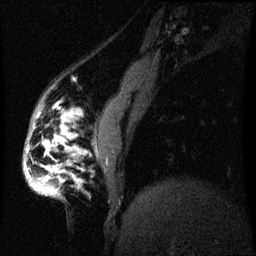
Breast MRI (dynamic contrast-enhanced), one sagittal slice; position 11 of 60 along the scan axis; dynamic contrast-enhanced series, image 2 of 3 at this slice position (ordered by acquisition); 1.5 T; TE 4.2 ms, TR 8 ms; 2.2 mm slice thickness; 256 × 256 image matrix. Female patient, age 50 years.
Outlined on this slice (semi-automatically segmented with operator editing):
- analysis volume of interest (the breast-tissue region the enhancement analysis was run in; not a lesion): box from (x=22, y=112) to (x=69, y=197) px
- tumour enhancement mask (voxels above the 70 % enhancement threshold inside the analysis volume of interest): (x=25, y=138)–(x=61, y=191)